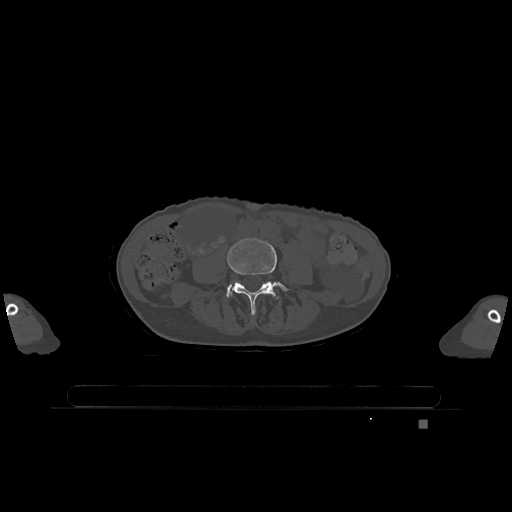
CT including the spine, one axial slice. Slice 293 of 1317 in the series (ordered by position). Bone window (W 1800 / L 400 HU). 0.5 mm slice thickness. 512 × 512 image matrix, field of view 500 × 500 mm. Patient: female, 74 years. From the clinical record (not read from this slice): primary cancer: lung; vertebrae with lytic lesions (as recorded): T1, T4, T5, T6, L4, L5.
Structures marked on this image (semi-automatic segmentation, software-assisted and operator-edited):
- L4 vertebra: box from (x=227, y=238) to (x=289, y=315) px
- L5 vertebra: (x=227, y=286)–(x=278, y=298)